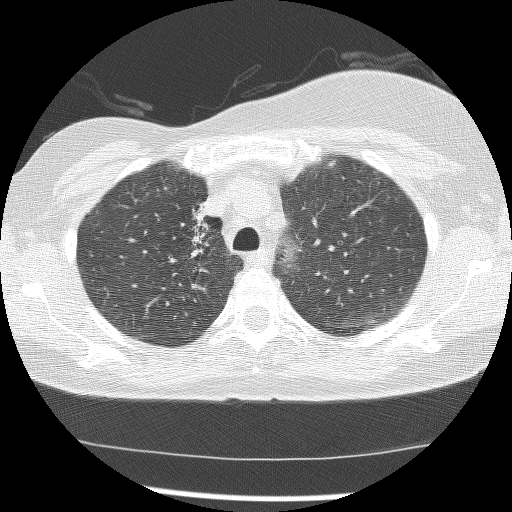
Chest CT (low-dose screening protocol), one axial image. First (baseline) screen. Lung window (W 1500 / L -600 HU). 512 × 512 image matrix. Female participant, aged 56 years at enrolment. Current smoker at enrolment.
- Expert reader's lesion annotation, bounding box (x1, y1, x2, y2) in pixels: (165, 195, 223, 273).
- The screening reader recorded 2 non-calcified nodules or masses ≥4 mm on this exam; which of them this box marks is not recorded.
- Lung cancer was diagnosed 1185 days after this screen (after the third annual screen): adenocarcinoma, NOS, right upper lobe, stage IIIB (AJCC 6th edition), 8 mm at pathology.